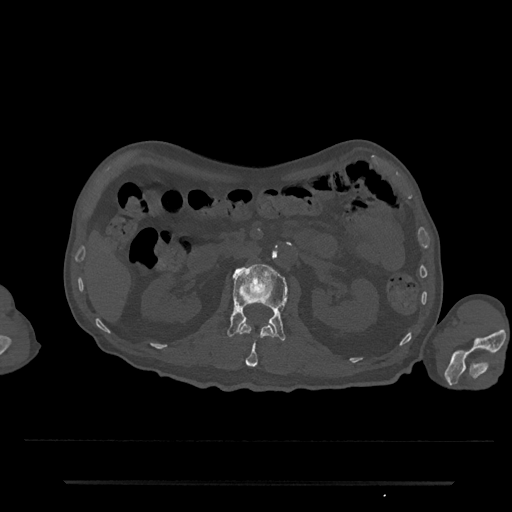
CT including the spine, one axial slice. Position 89 of 797 along the scan axis. 120 kVp. Bone window (W 1800 / L 400 HU). 512 × 512 image matrix. Male patient, age 74 years. From the clinical record (not read from this slice): primary cancer: prostate.
Structures marked on this image (semi-automatically segmented with operator editing):
- L1 vertebra: bounding box <239,322,274,367> (left, top, right, bottom; pixels)
- L2 vertebra: <227,263,288,341>